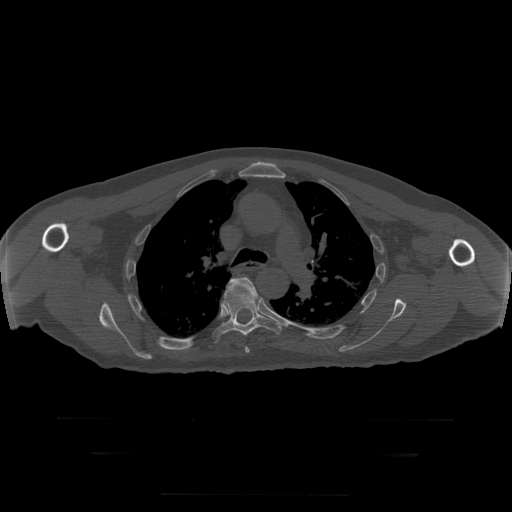
CT including the spine, one axial slice. Slice 212 of 397 in the series (ordered by position). 120 kVp. Bone window (W 1800 / L 400 HU). 1.25 mm slice thickness. 512 × 512 image matrix, field of view 510 × 510 mm. Patient age 73 years. From the clinical record (not read from this slice): primary cancer: prostate.
Structures marked on this image (semi-automatically segmented with operator editing):
- T5 vertebra: bounding box [x1, y1, x2, y2] px = [230, 278, 258, 353]
- T6 vertebra: [214, 286, 282, 342]